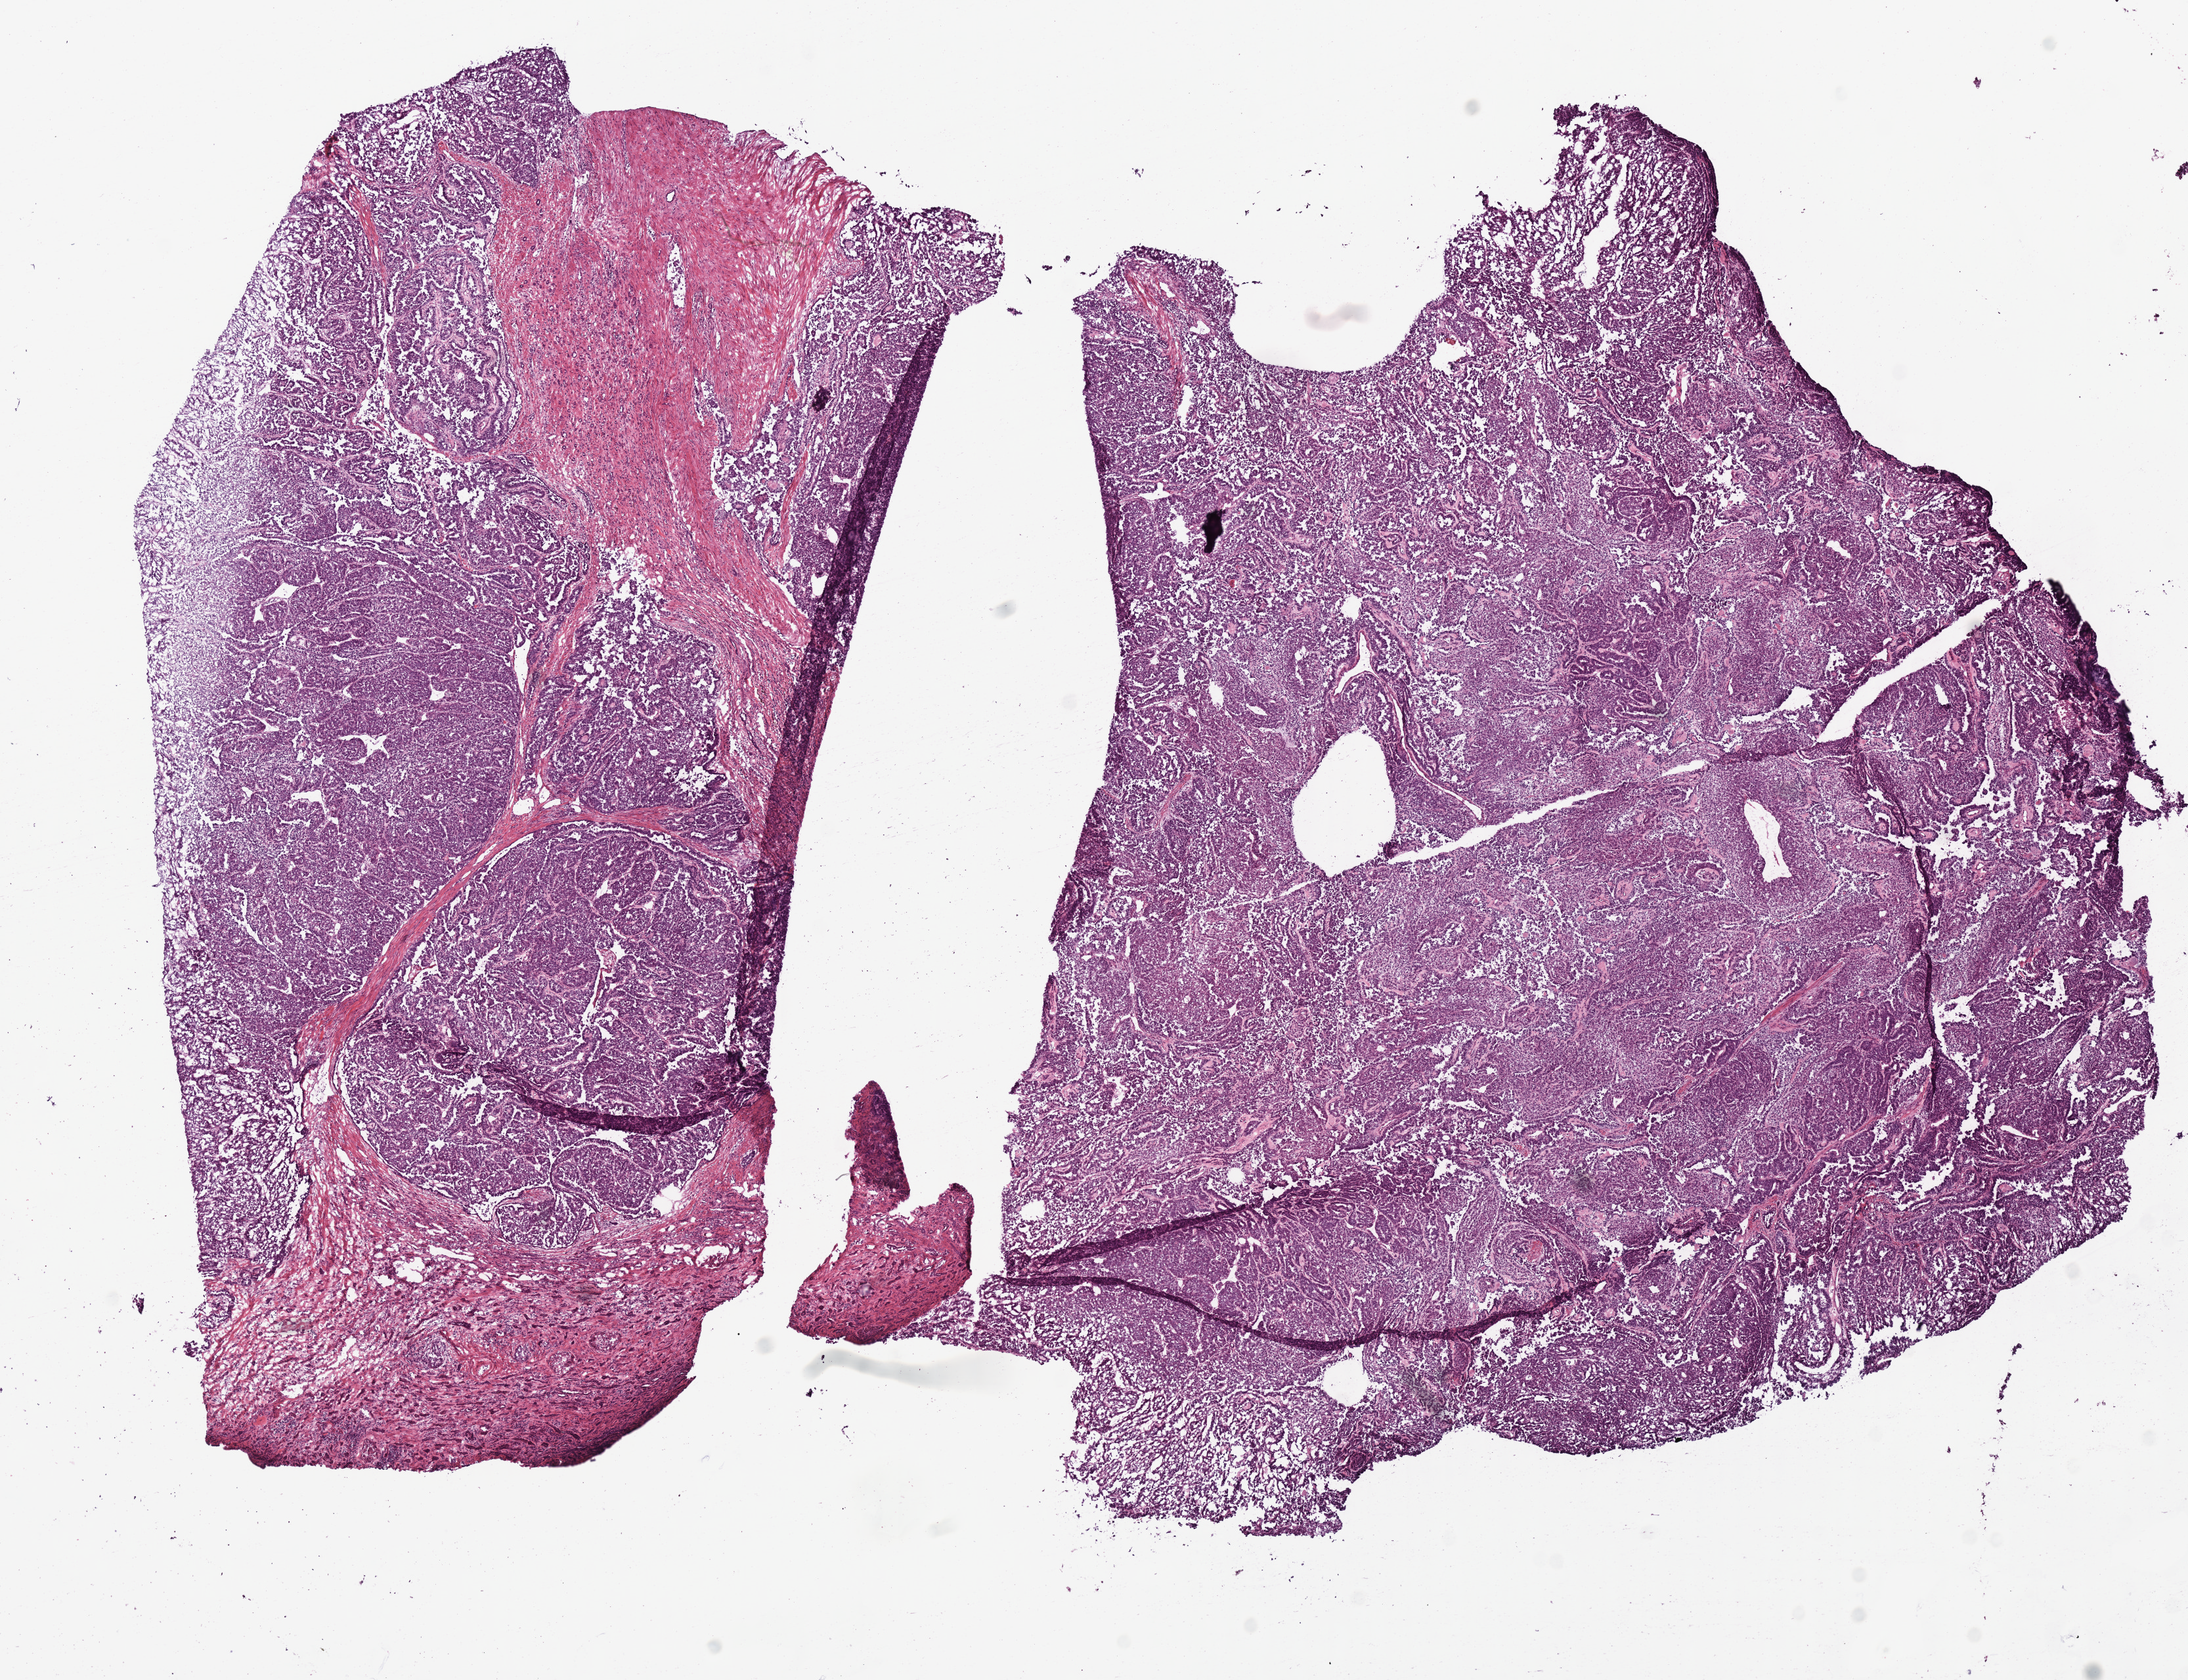
Whole-slide histology image, Hematoxylin and eosin (H&E) stained, low-resolution overview of the scanned area, about 13.1 x 10.1 mm, frozen section from the top of the tissue portion, primary tumour sample from the kidney. Patient: female, age at initial diagnosis 55 years. Slide review estimates, as recorded: tumour cells 85%, tumour nuclei 85%.
Pathologic diagnosis: Papillary adenocarcinoma, NOS.